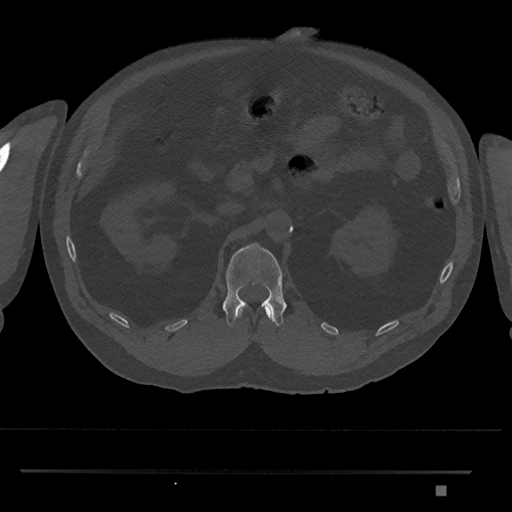
CT including the spine, one axial slice; slice 837 of 1134 in the series (ordered by position); 120 kVp; bone window (W 1800 / L 400 HU); 512 × 512 image matrix, field of view 429 × 429 mm. Patient: male, 65 years. Case-level facts recorded for this patient, not image findings: primary cancer: prostate.
Annotated regions visible in this slice (semi-automatic segmentation, software-assisted and operator-edited):
- L1 vertebra: bounding box <223,243,287,327> (left, top, right, bottom; pixels)
- T12 vertebra: <237,308,271,319>